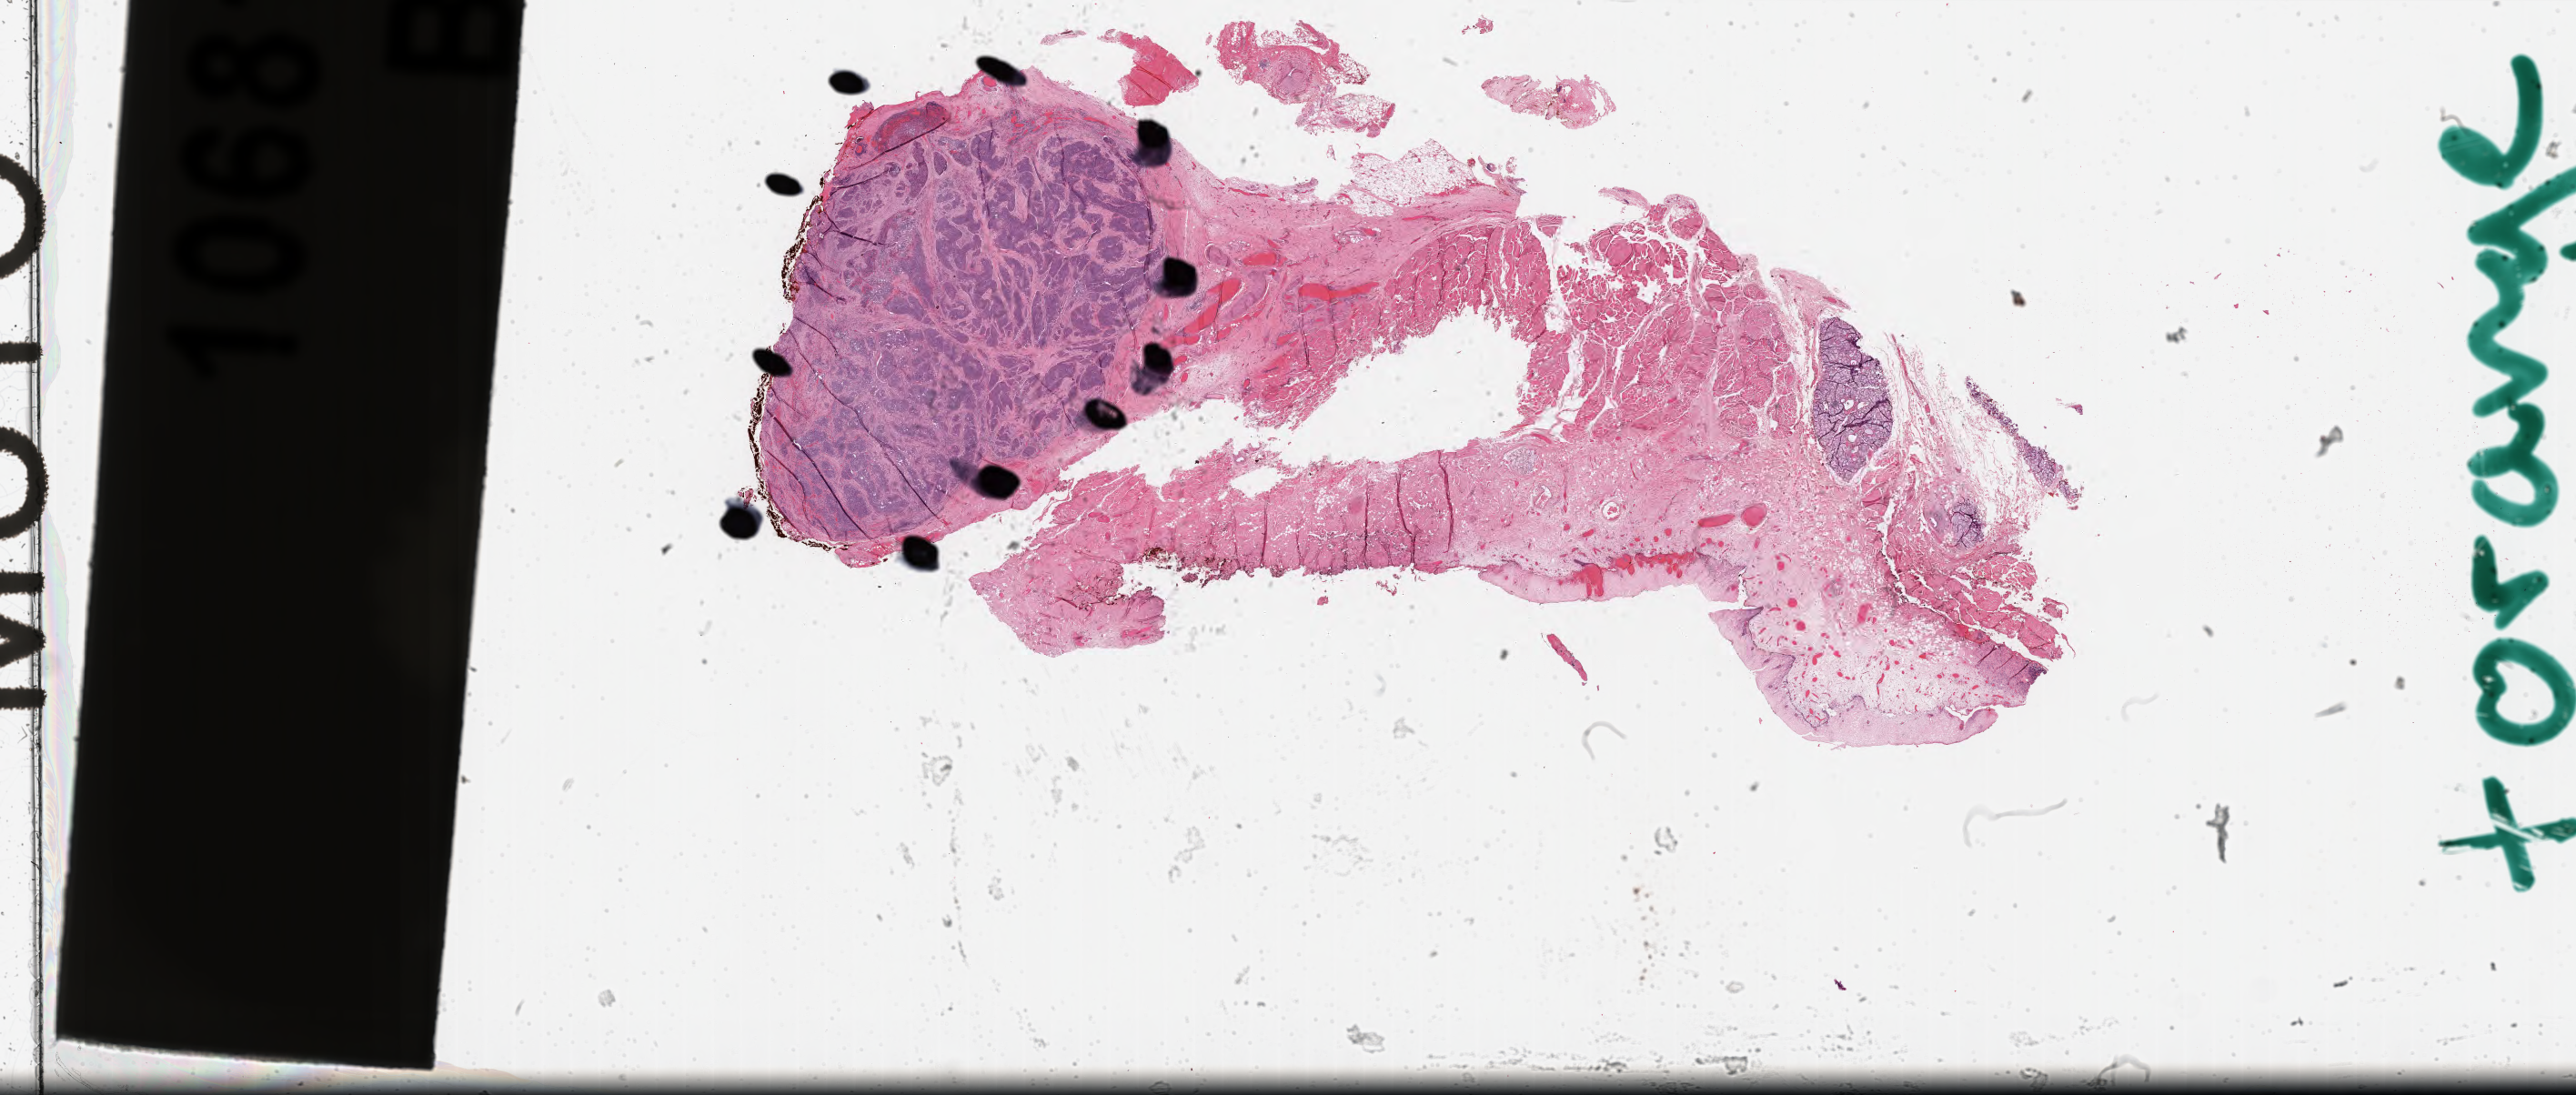
Whole-slide histology image, Hematoxylin and eosin (H&E) stained — whole scanned area (about 44.6 x 19.0 mm) shown as a low-resolution overview; FFPE section; primary tumour sample from the head and neck. Patient: male, age at initial diagnosis 53 years. Histologic grade: G3 (poorly differentiated).
AJCC pathologic stage: IVA (6th edition). TNM: T4a NX MX. Diagnosis: Squamous cell carcinoma, NOS (lower gum). Laterality: right.